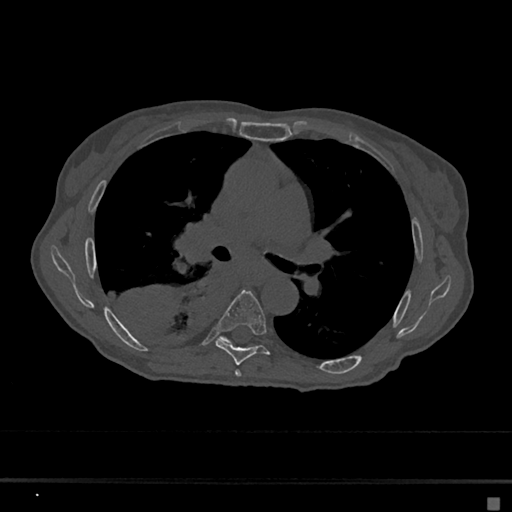
CT including the spine, one axial slice; position 413 of 797 along the scan axis; bone window (W 1800 / L 400 HU); 0.5 mm slice thickness; 512 × 512 image matrix, field of view 360 × 360 mm. Female patient, age 68 years. From the clinical record (not read from this slice): primary cancer: renal.
Annotated regions visible in this slice (semi-automatically segmented with operator editing):
- T5 vertebra: bounding box (x1, y1, x2, y2) in pixels: (235, 370, 242, 377)
- T6 vertebra: (215, 290, 271, 365)
- T7 vertebra: (222, 337, 231, 343)